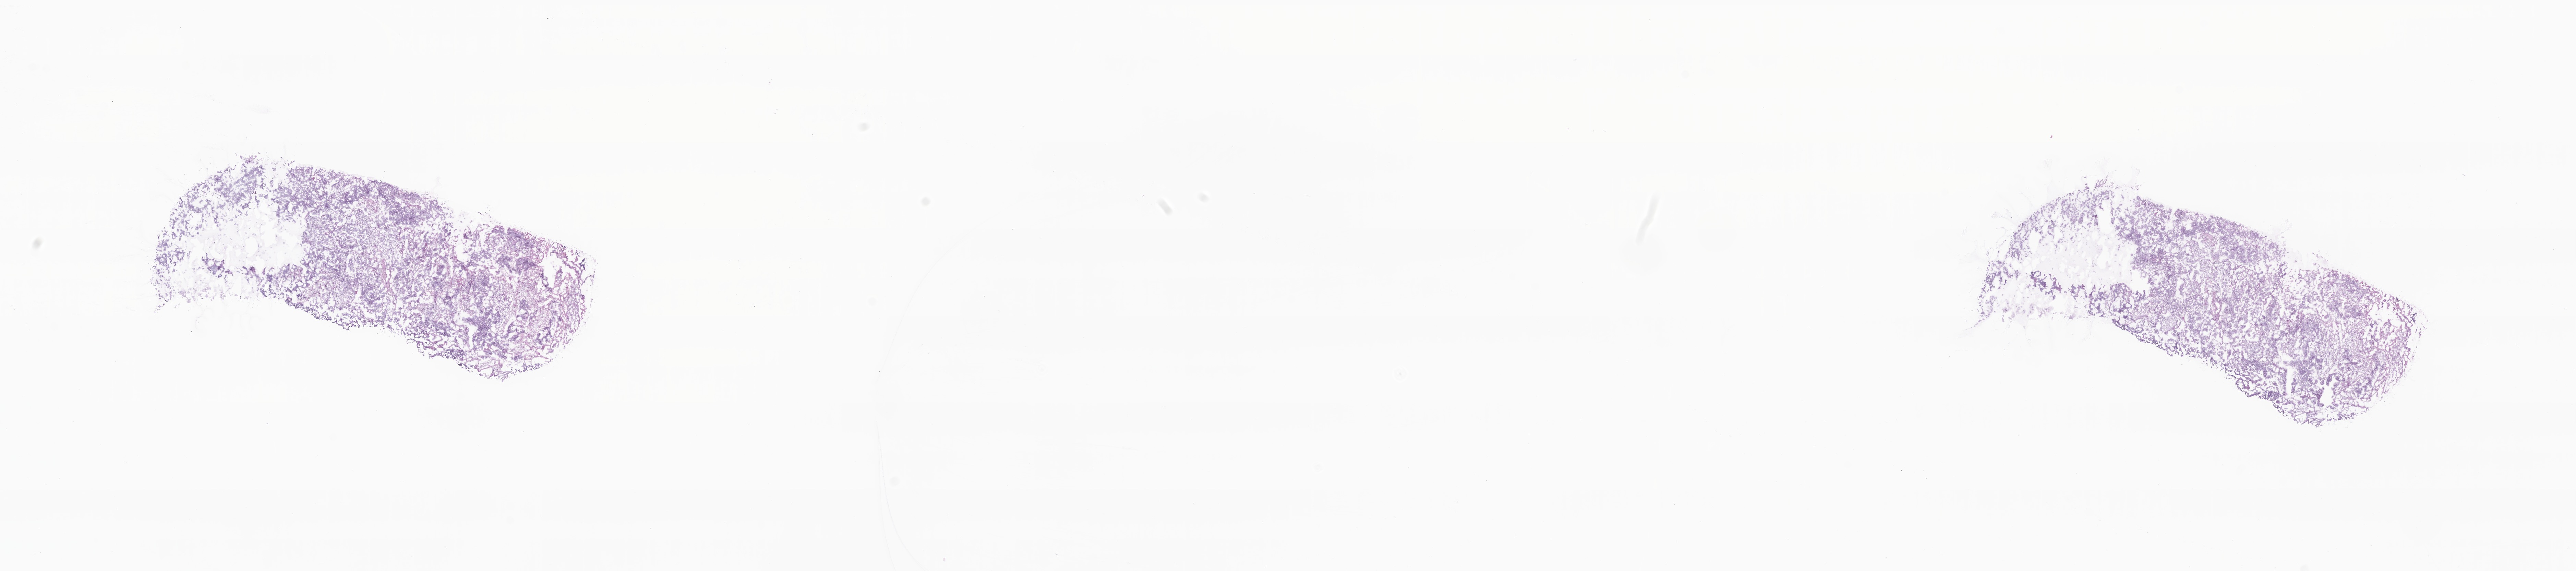
Digitized H&E-stained section — whole scanned area (about 31.7 x 7.0 mm) shown as a low-resolution overview. Cryosection. Primary tumor. Site: endometrium. Patient sex: female. Pathologist review of this section (percent, as recorded): tumor cells 90%, tumor nuclei 90%, stromal cells 10%, necrosis 0%, normal cells 0%. Inflammatory infiltration, as recorded: lymphocyte infiltration 2%, monocyte infiltration 2%, neutrophil infiltration 3%.
AJCC pathologic stage: Stage IIIC1. Histologic diagnosis: High grade serous carcinoma. Section: bottom of the tissue portion.